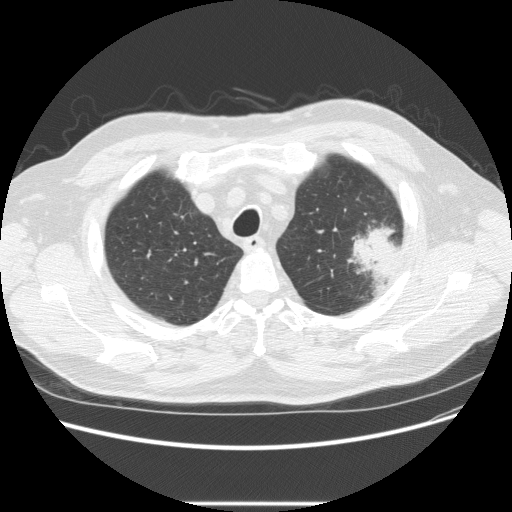
Low-dose screening chest CT, axial slice, baseline annual screen, lung window (W 1500 / L -600 HU), 2.5 mm slice thickness, slice 46 of 233 in the series, 512 × 512 image matrix, field of view 380 × 380 mm. Male participant, aged 73 years at enrolment. Former smoker at enrolment.
• Lesion marked by an expert reader, bounding box (x1, y1, x2, y2) in pixels: (332, 216, 409, 284).
• The screening reader recorded 2 non-calcified nodules or masses ≥4 mm on this exam (left upper lobe, right upper lobe); which of them this box marks is not recorded.
• Official screen result: positive, change unspecified: nodule(s) >= 4 mm or enlarging nodule(s), mass(es), or other non-specific abnormalities suspicious for lung cancer.
• Later outcome: lung cancer diagnosed 11 days after this screen — bronchiolo-alveolar adenocarcinoma, NOS, other location, well differentiated (G1), stage IV (AJCC 6th edition).